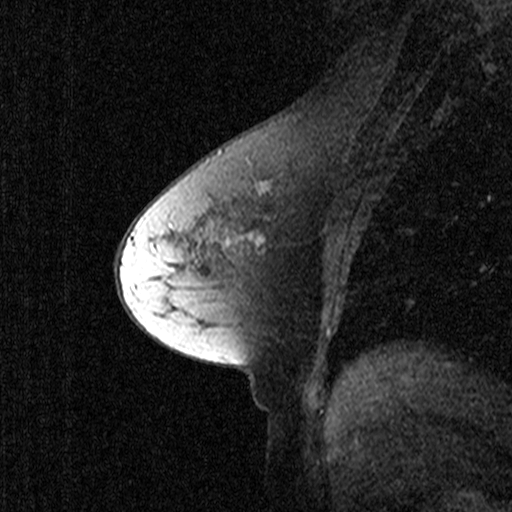
Breast MRI (dynamic contrast-enhanced), one sagittal slice; slice 22 of 44 in the series (ordered by position); dynamic contrast-enhanced study with each time point stored as its own series, time point 2 of 3 at this slice position (early post-contrast, ordered by acquisition time); 1.5 T; TE 4.5 ms, TR 11 ms; 2.27 mm slice thickness; 512 × 512 image matrix, field of view 200 × 200 mm. Patient: female, 53 years. Case-level facts recorded for this patient, not image findings: setting: breast cancer imaged before/during neoadjuvant chemotherapy; receptor status: HR-positive, HER2-negative.
Structures marked on this image (semi-automatic segmentation, software-assisted and operator-edited):
- analysis volume of interest (the breast-tissue region the enhancement analysis was run in; not a lesion): bounding box <192,146,303,281> (left, top, right, bottom; pixels)
- tumour enhancement mask (voxels above the 90 % enhancement threshold inside the analysis volume of interest): <249,183,270,244>